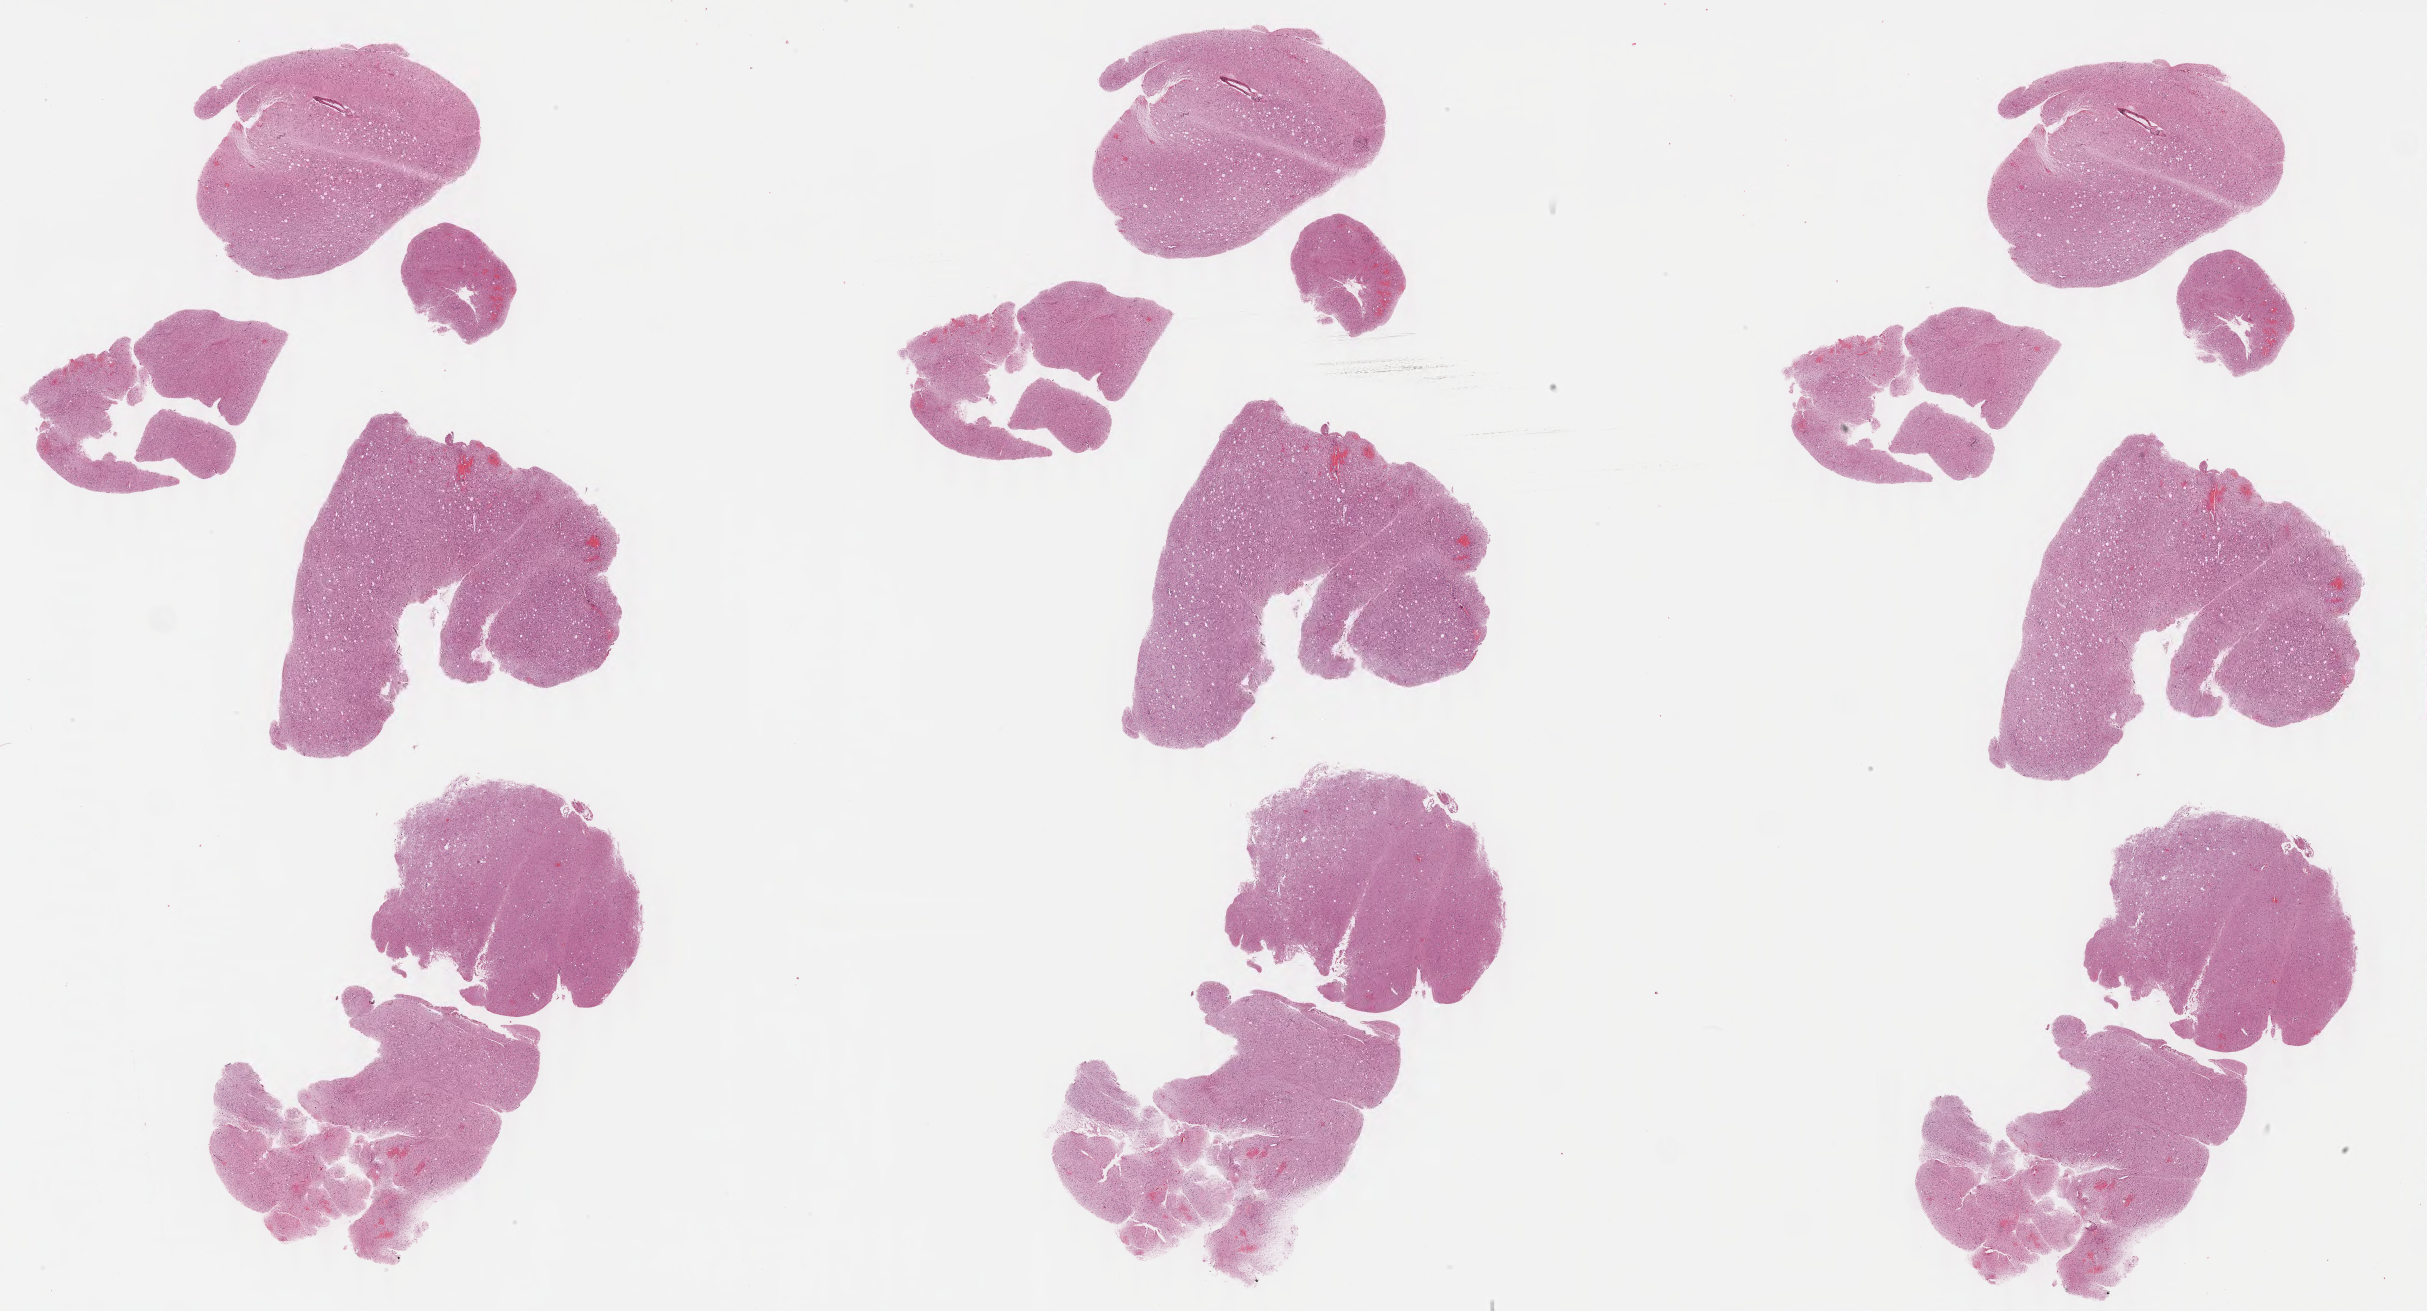
Digitized H&E tissue section (whole slide), shown as a low-resolution overview of the whole scanned area (about 38.4 x 20.7 mm, acquisition: 40x scan). Formalin-fixed paraffin-embedded (FFPE) diagnostic section. Primary tumour sample from the brain. Patient: male, age at initial diagnosis 20 years. Histologic grade: G2 (moderately differentiated).
• diagnosis: Mixed glioma (cerebrum)